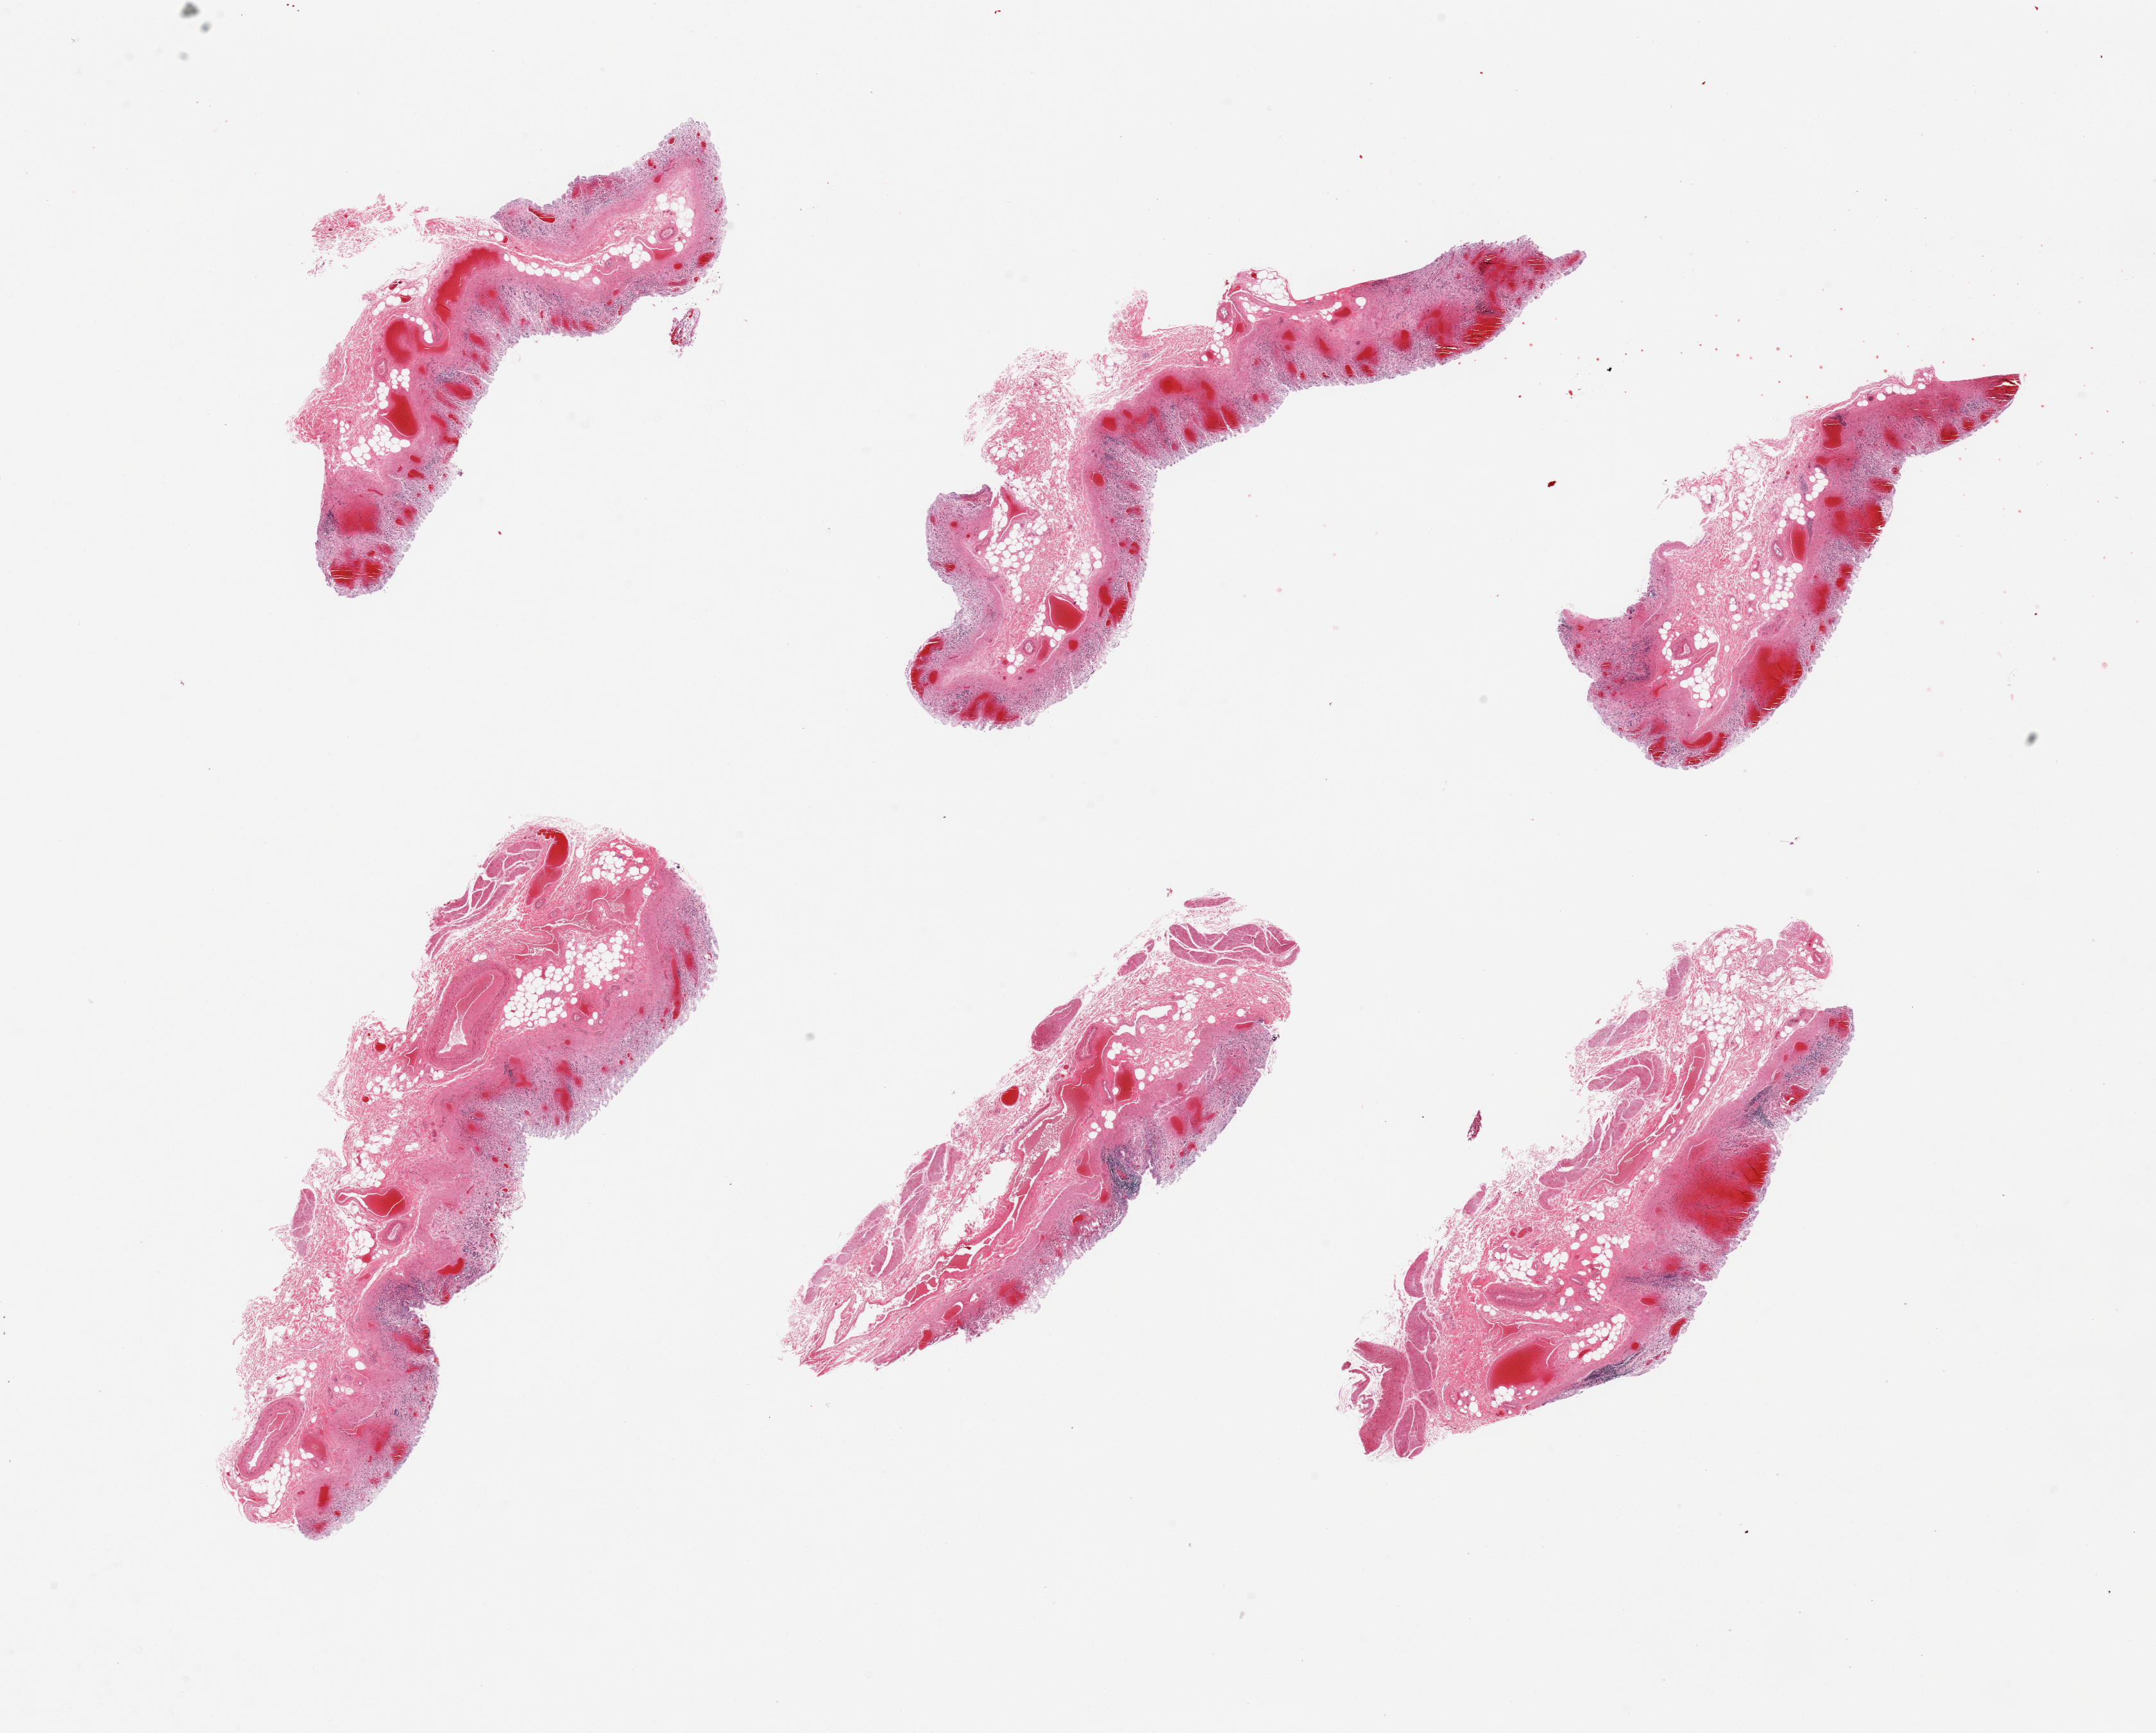
Whole-slide image, haematoxylin and eosin stain — shown as a low-resolution overview of the whole scanned area (about 26.6 x 21.4 mm). PAXgene-fixed paraffin-embedded (PFPE) section. Sampled site (target tissue): stomach. Donor tissue sample.
* pathologist's review note for this sample: 6 pieces, marked autolysis, congestion